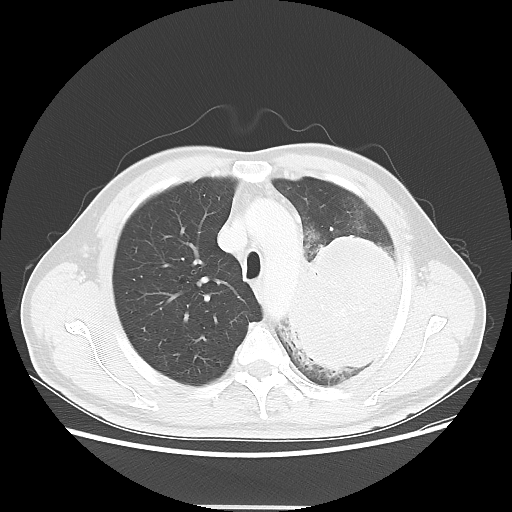
Chest CT, one axial slice; reconstruction kernel LUNG; 100 kVp; lung window (W 1500 / L -600 HU); 5 mm slice thickness; 512 × 512 image matrix. Patient: male, 60 years. From the clinical record (not read from this slice): clinical TNM (as recorded): T4 N1 M1a.
Structures marked on this image (rectangle marked by the reading radiologist):
- lung tumour (recorded histology: large cell carcinoma): box from (x=275, y=233) to (x=410, y=377) px